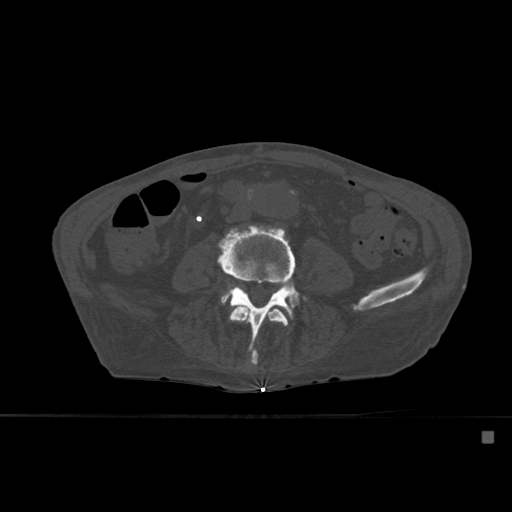
CT including the spine, one axial slice; position 195 of 527 along the scan axis; bone window (W 1800 / L 400 HU); 1.5 mm slice thickness; 512 × 512 image matrix, field of view 373 × 373 mm. Male patient, age 78 years. From the clinical record (not read from this slice): primary cancer: prostate.
Structures marked on this image (semi-automatic segmentation, software-assisted and operator-edited):
- L3 vertebra: bounding box [x1, y1, x2, y2] px = [229, 306, 288, 367]
- L4 vertebra: [218, 227, 308, 353]
- L5 vertebra: [222, 291, 231, 303]